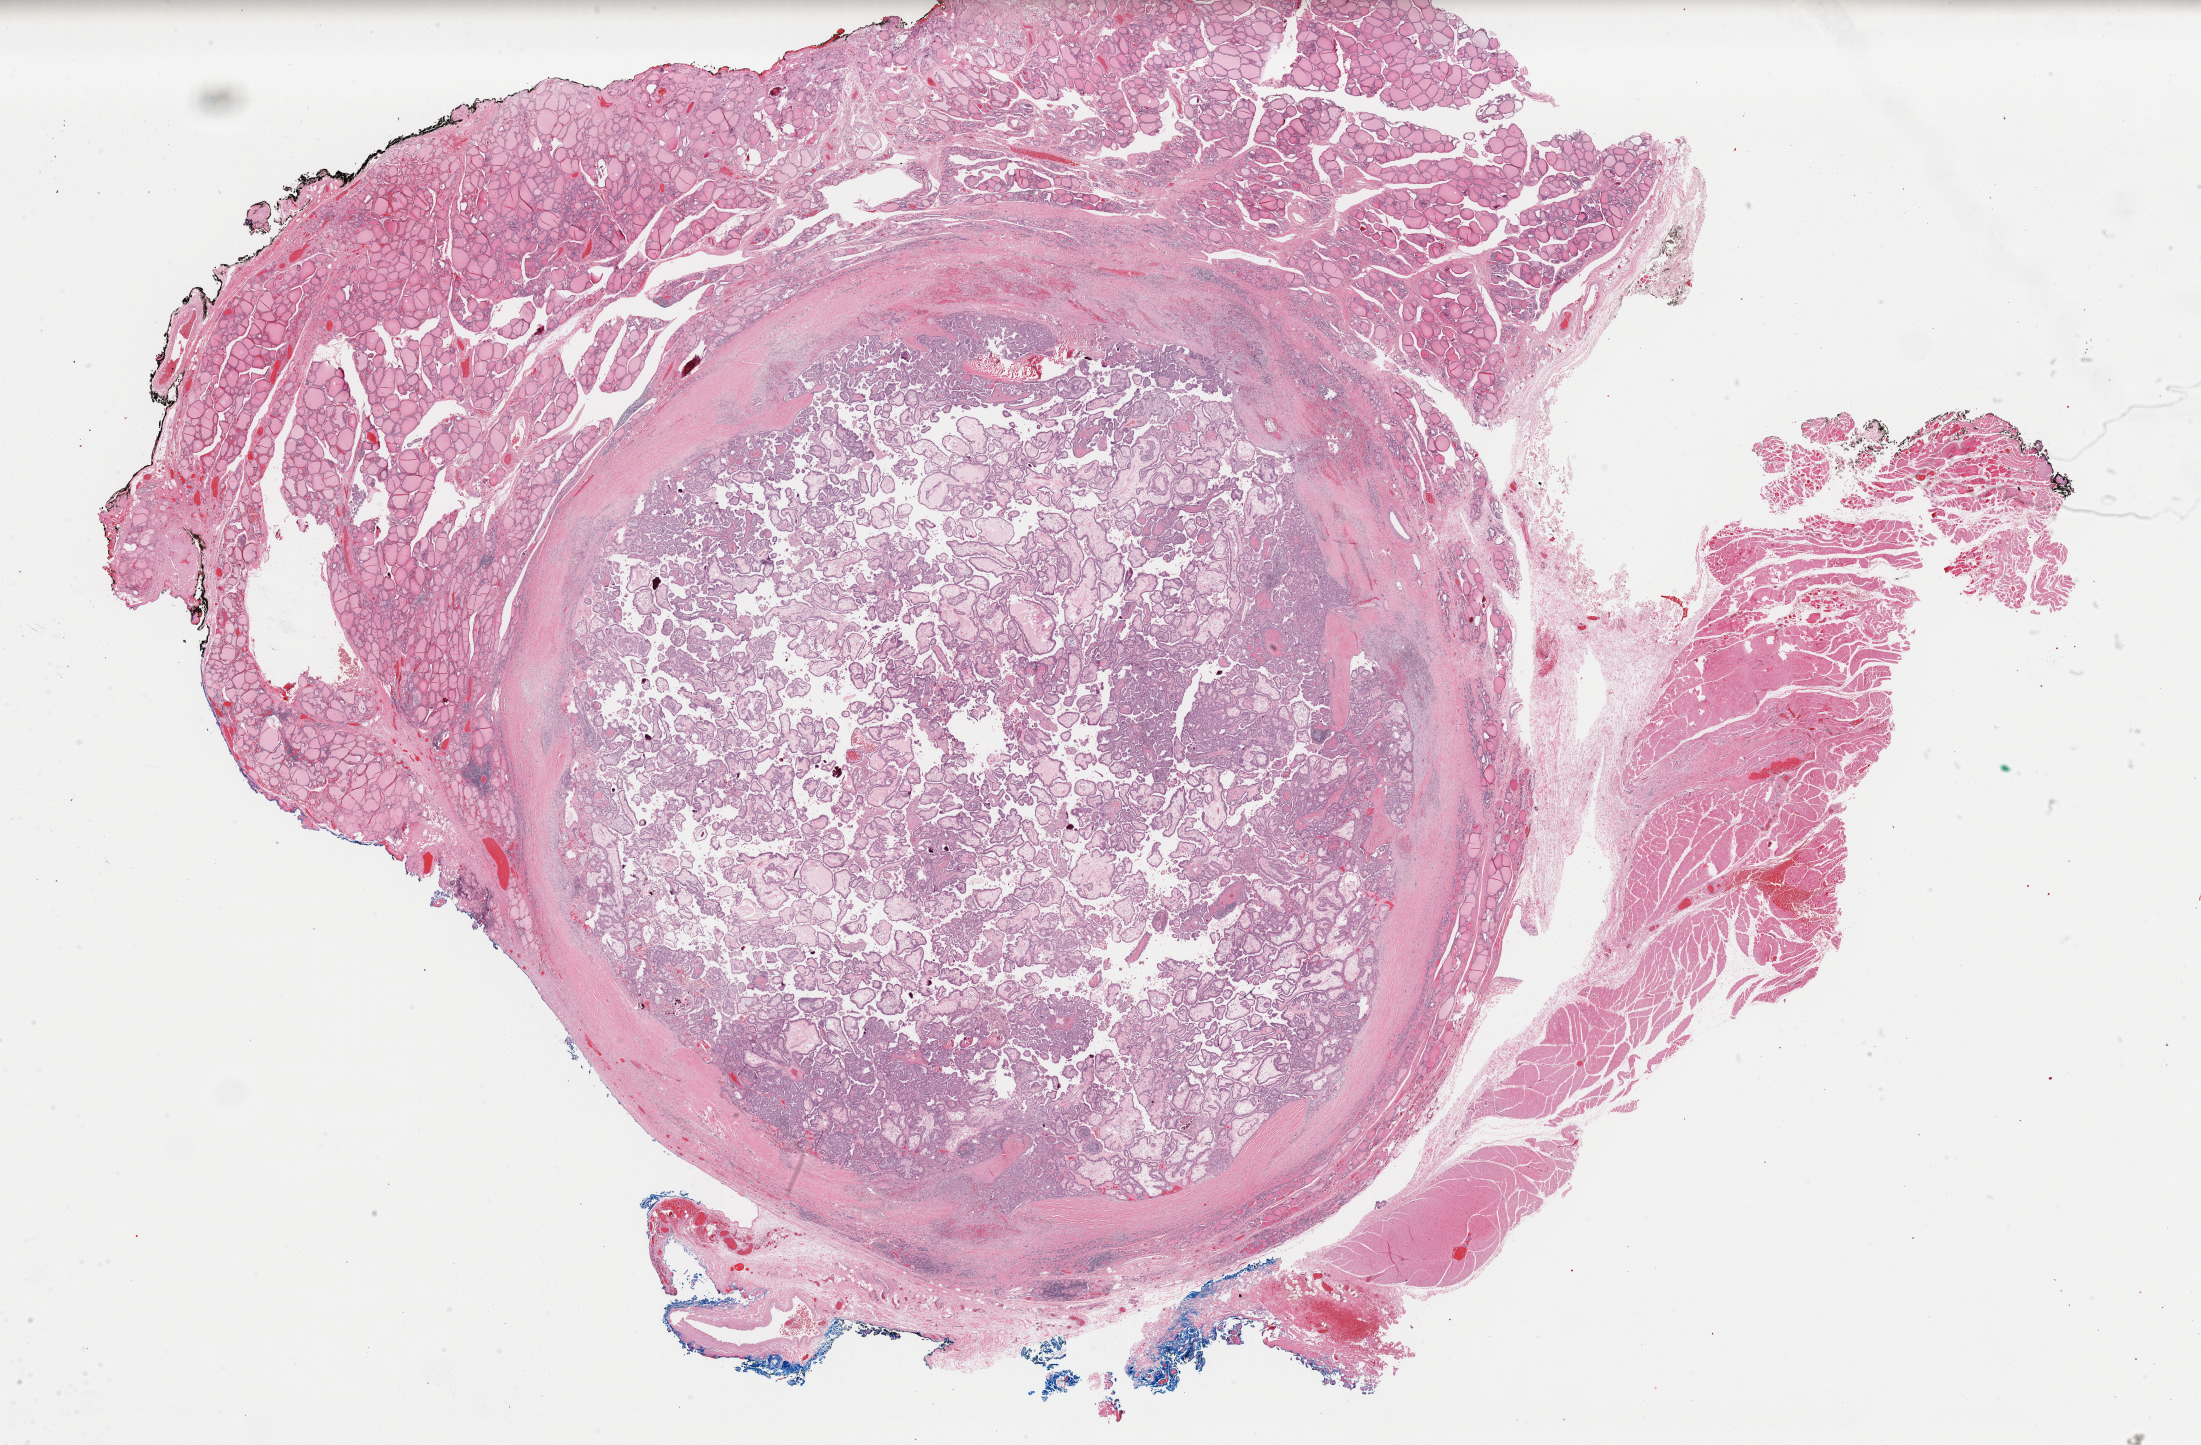
Digitized Hematoxylin and eosin (H&E) stained tissue section (whole slide) — a low-resolution overview of the entire scanned area, about 34.7 x 22.8 mm; FFPE section; sample: primary tumour, thyroid. Female patient; age at initial diagnosis 38 years.
AJCC pathologic stage: I (7th edition). Diagnosis: Papillary adenocarcinoma, NOS (thyroid gland). Lymph nodes positive (case pathology): 0 of 1 examined.